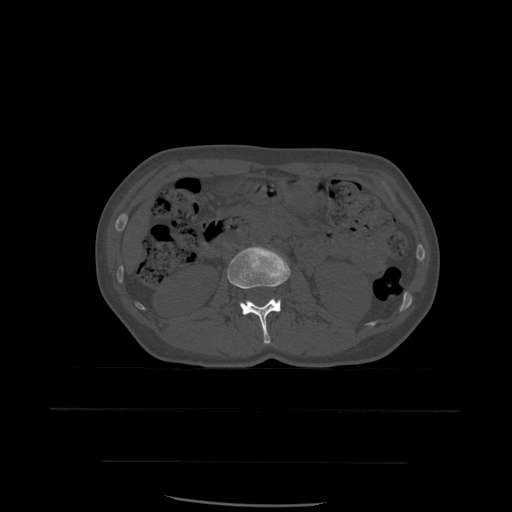
CT including the spine, one axial slice; slice 221 of 574 in the series (ordered by position); bone window (W 1800 / L 400 HU); 1.25 mm slice thickness; 512 × 512 image matrix, field of view 392 × 392 mm. Patient age 48 years. From the clinical record (not read from this slice): primary cancer: lung; vertebrae with lytic lesions (as recorded): T11.
Annotated regions visible in this slice (semi-automatic segmentation, software-assisted and operator-edited):
- L2 vertebra: box from (x=227, y=247) to (x=291, y=345) px